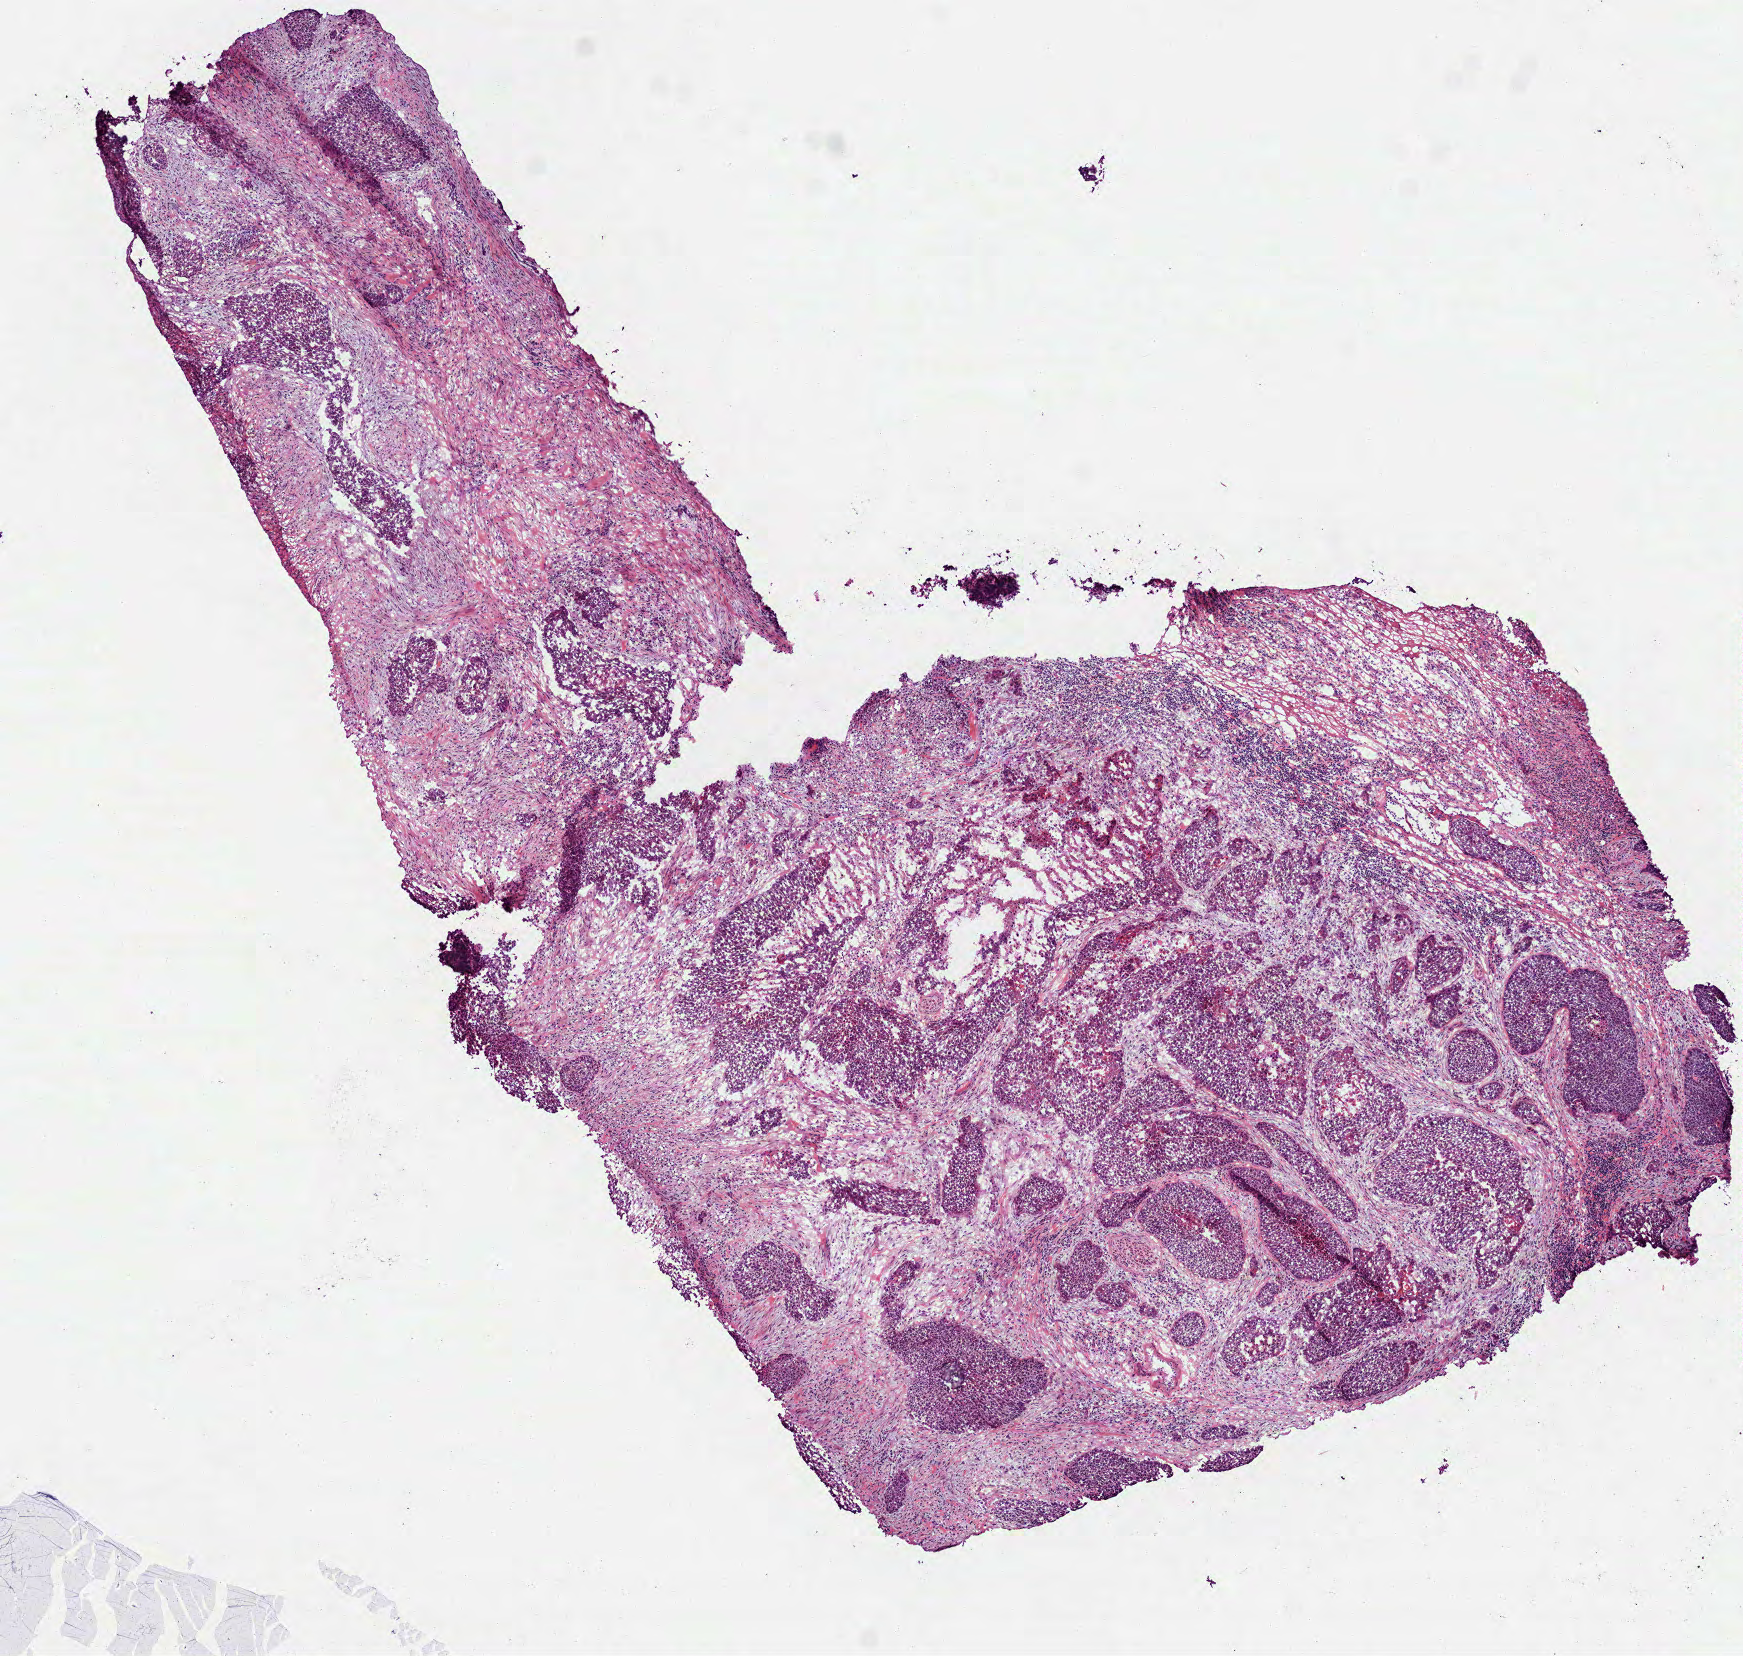
Whole-slide histology image, H&E-stained — shown as a low-resolution overview of the whole scanned area (about 7.0 x 6.7 mm, acquisition: 40x scan); frozen section from the bottom of the tissue portion; sample: primary tumour, head and neck. Male patient; age at initial diagnosis 66 years. Histologic grade: G3 (poorly differentiated). Slide review estimates, as recorded: tumour cells 60%, tumour nuclei 60%, normal cells 0%, stromal cells 40%, necrosis 10%.
* diagnosis: Squamous cell carcinoma, NOS
* AJCC pathologic stage: IVA (7th edition)
* TNM: T3 N2c
* lymph nodes positive (case pathology): 2 of 25 examined